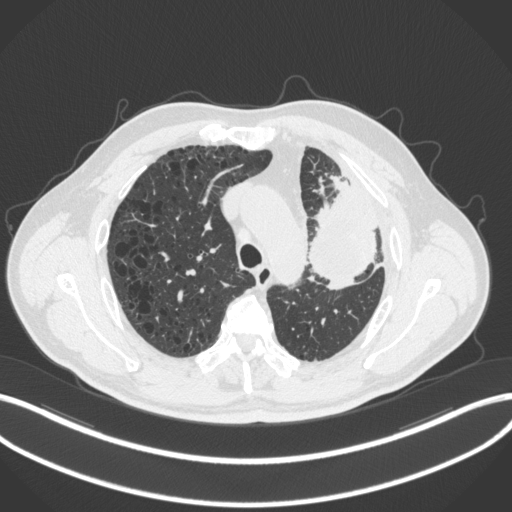
Chest CT, one axial slice; slice 220 of 286 in the series (ordered by position); reconstruction kernel B31f; 120 kVp; lung window (W 1500 / L -600 HU); 1 mm slice thickness; 512 × 512 image matrix, field of view 400 × 400 mm. Patient: male, 68 years. From the clinical record (not read from this slice): clinical TNM (as recorded): T3 N3 M1.
Outlined on this slice (bounding box drawn by a radiologist):
- lung tumour (recorded histology: adenocarcinoma): bounding box (x1, y1, x2, y2) in pixels: (305, 171, 383, 294)